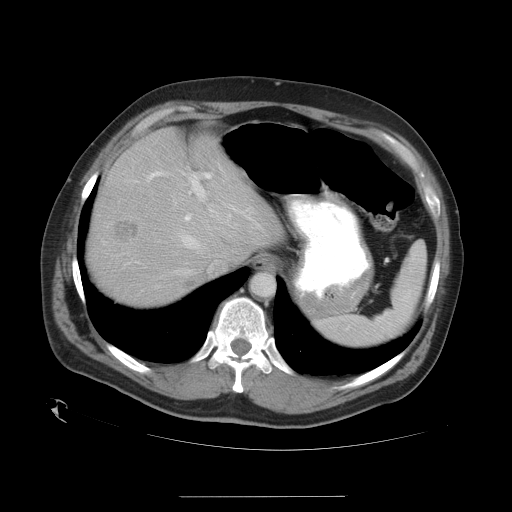
Contrast-enhanced abdominal CT, one axial slice. Slice 26 of 35 in the series (ordered by position). 120 kVp. Soft-tissue window (W 400 / L 40 HU). 7.5 mm slice thickness. 512 × 512 image matrix, field of view 450 × 450 mm. Male patient, age 67 years. Case-level facts recorded for this patient, not image findings: diagnosis: colorectal cancer liver metastases, imaged before liver resection; multiple liver metastases: no; largest metastasis: 2.3 cm.
Structures marked on this image (manually delineated by an expert):
- hepatic veins: bounding box [x1, y1, x2, y2] px = [124, 172, 210, 275]
- liver: [90, 131, 279, 304]
- planned liver remnant (the part of the liver to remain after resection): [98, 131, 279, 304]
- portal vein (with intrahepatic branches): [149, 171, 260, 227]
- liver metastasis: [115, 222, 141, 243]